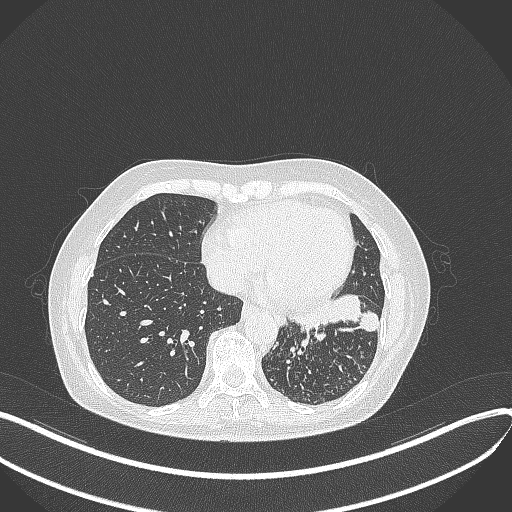
Chest CT, one axial slice; slice 138 of 429 in the series (ordered by position); reconstruction kernel B70f; 100 kVp; lung window (W 1500 / L -600 HU); 1 mm slice thickness; 512 × 512 image matrix. Patient: female, 63 years. From the clinical record (not read from this slice): clinical TNM (as recorded): T1b N0 M0.
Structures marked on this image (bounding box drawn by a radiologist):
- lung tumour (recorded histology: adenocarcinoma): bounding box [x1, y1, x2, y2] px = [290, 293, 382, 344]